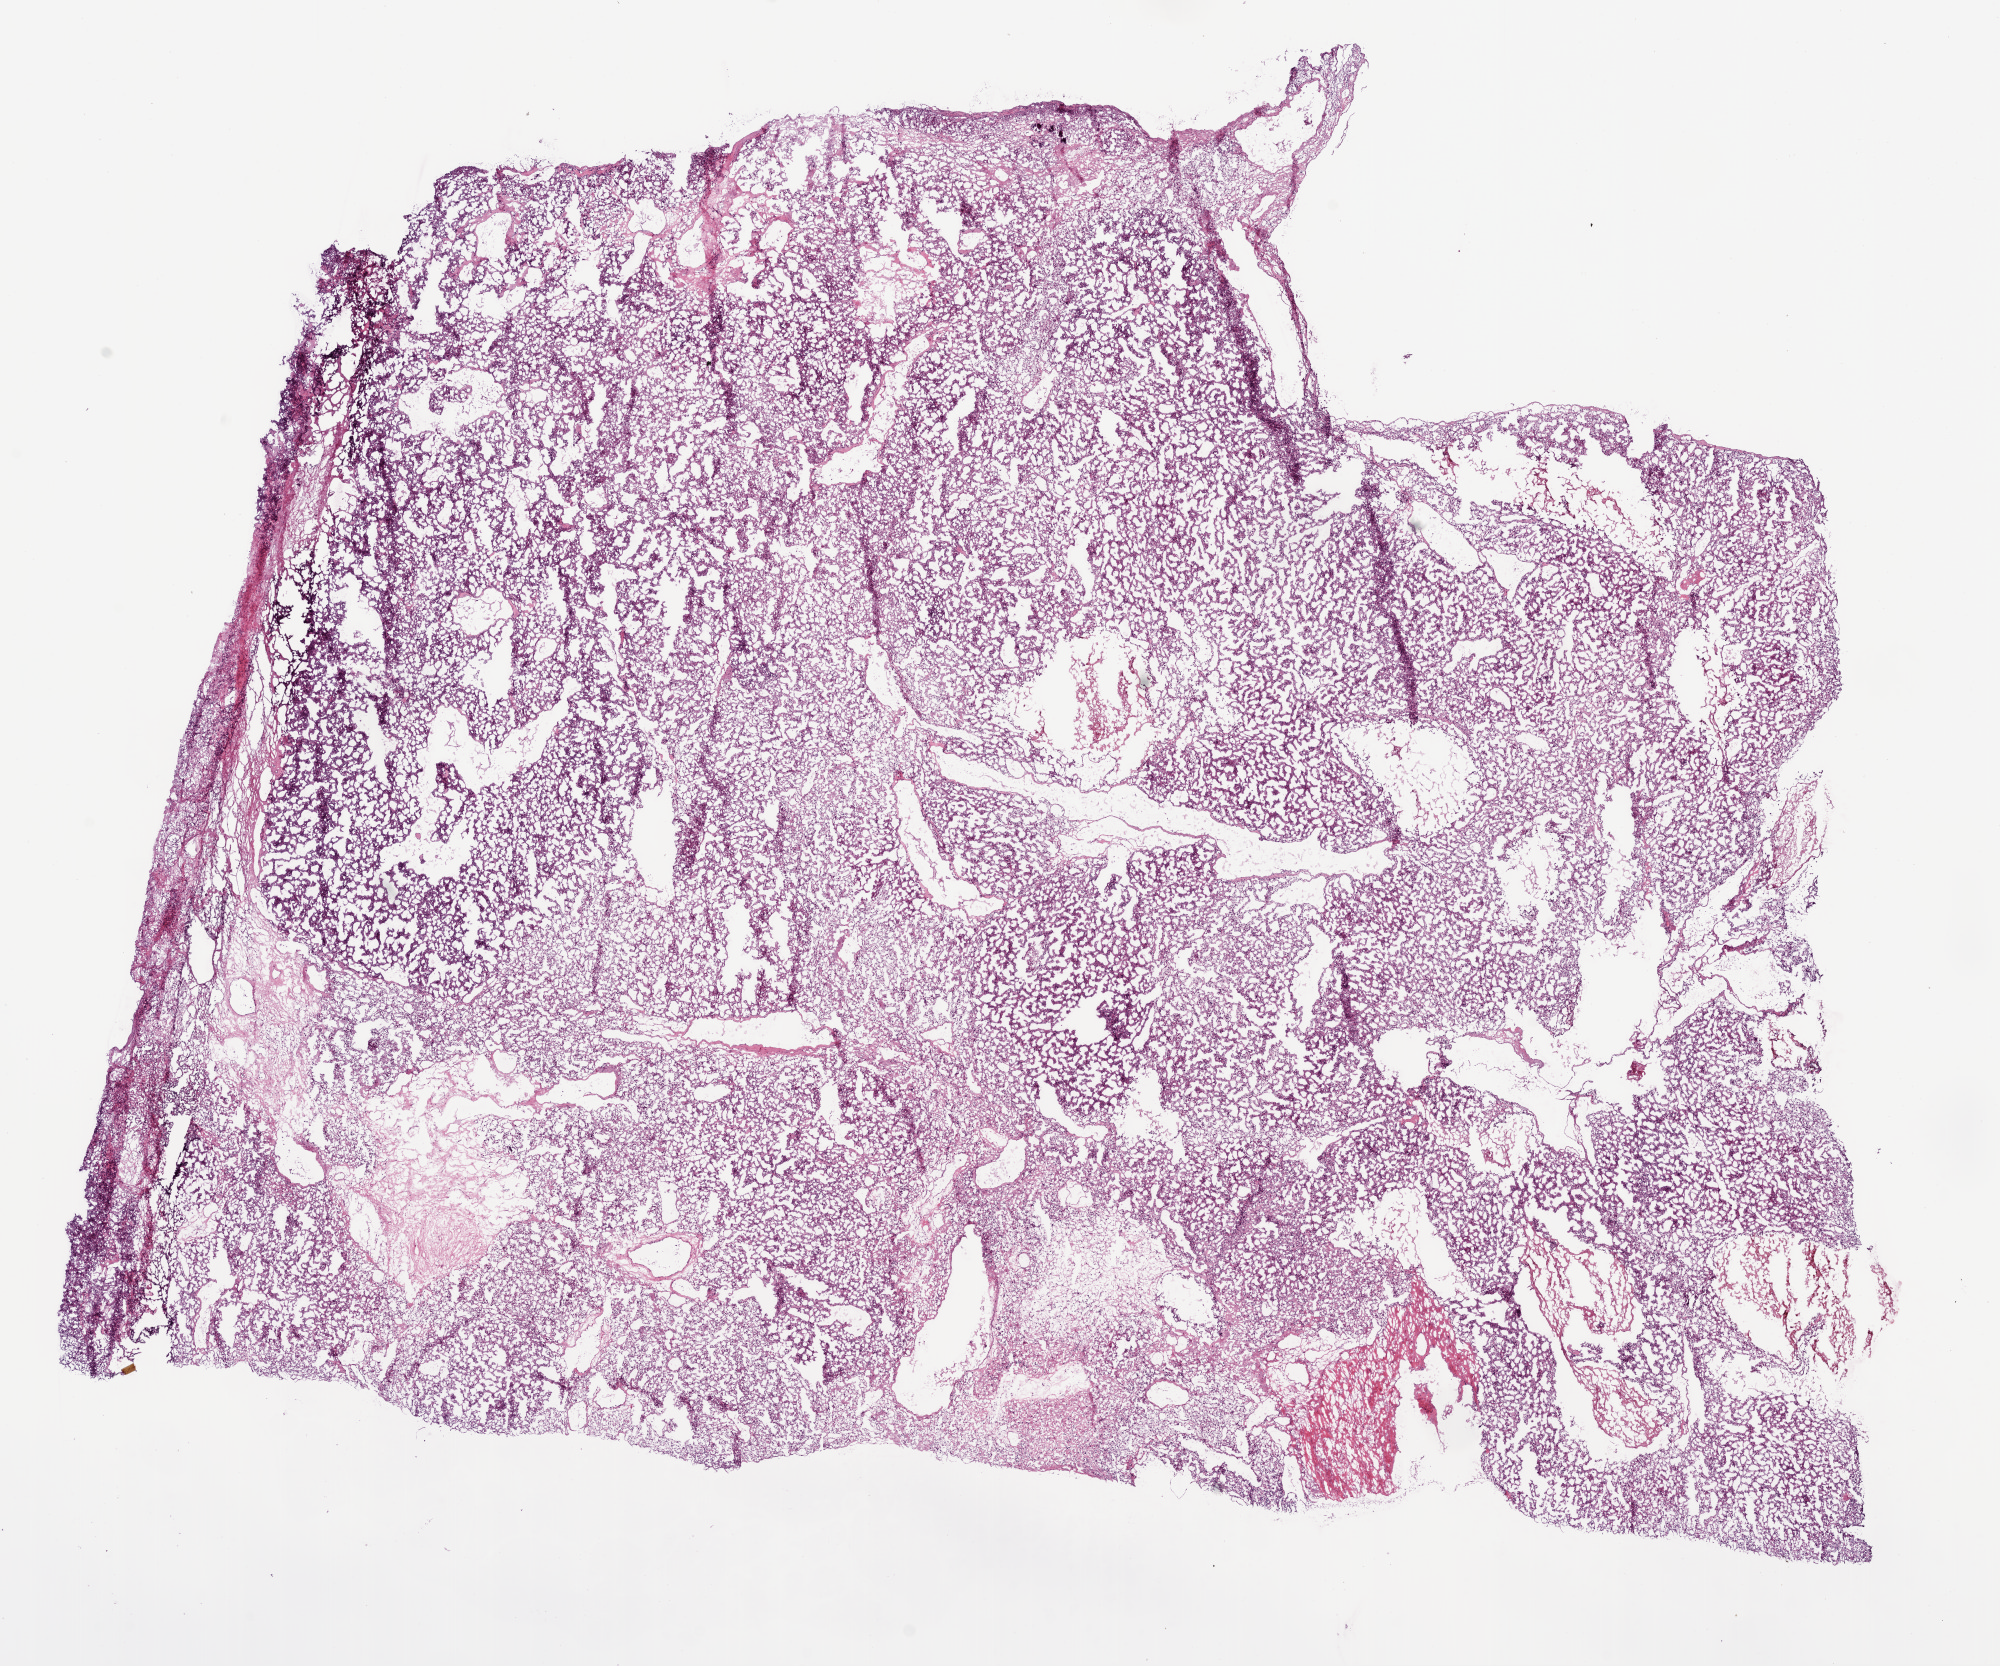
Hematoxylin and eosin (H&E) stained whole-slide image, a low-resolution overview of the entire scanned area, about 16.0 x 13.4 mm. Frozen section. Sample: primary tumour, kidney. Patient: male, age at initial diagnosis 63 years. Histologic grade: G4 (undifferentiated). Slide review estimates, as recorded: tumour cells 95%, tumour nuclei 90%, normal cells 0%, stromal cells 5%, necrosis 0%.
* diagnosis: Clear cell adenocarcinoma, NOS
* lymph nodes positive (case pathology): 0 of 4 examined
* AJCC pathologic stage: IV